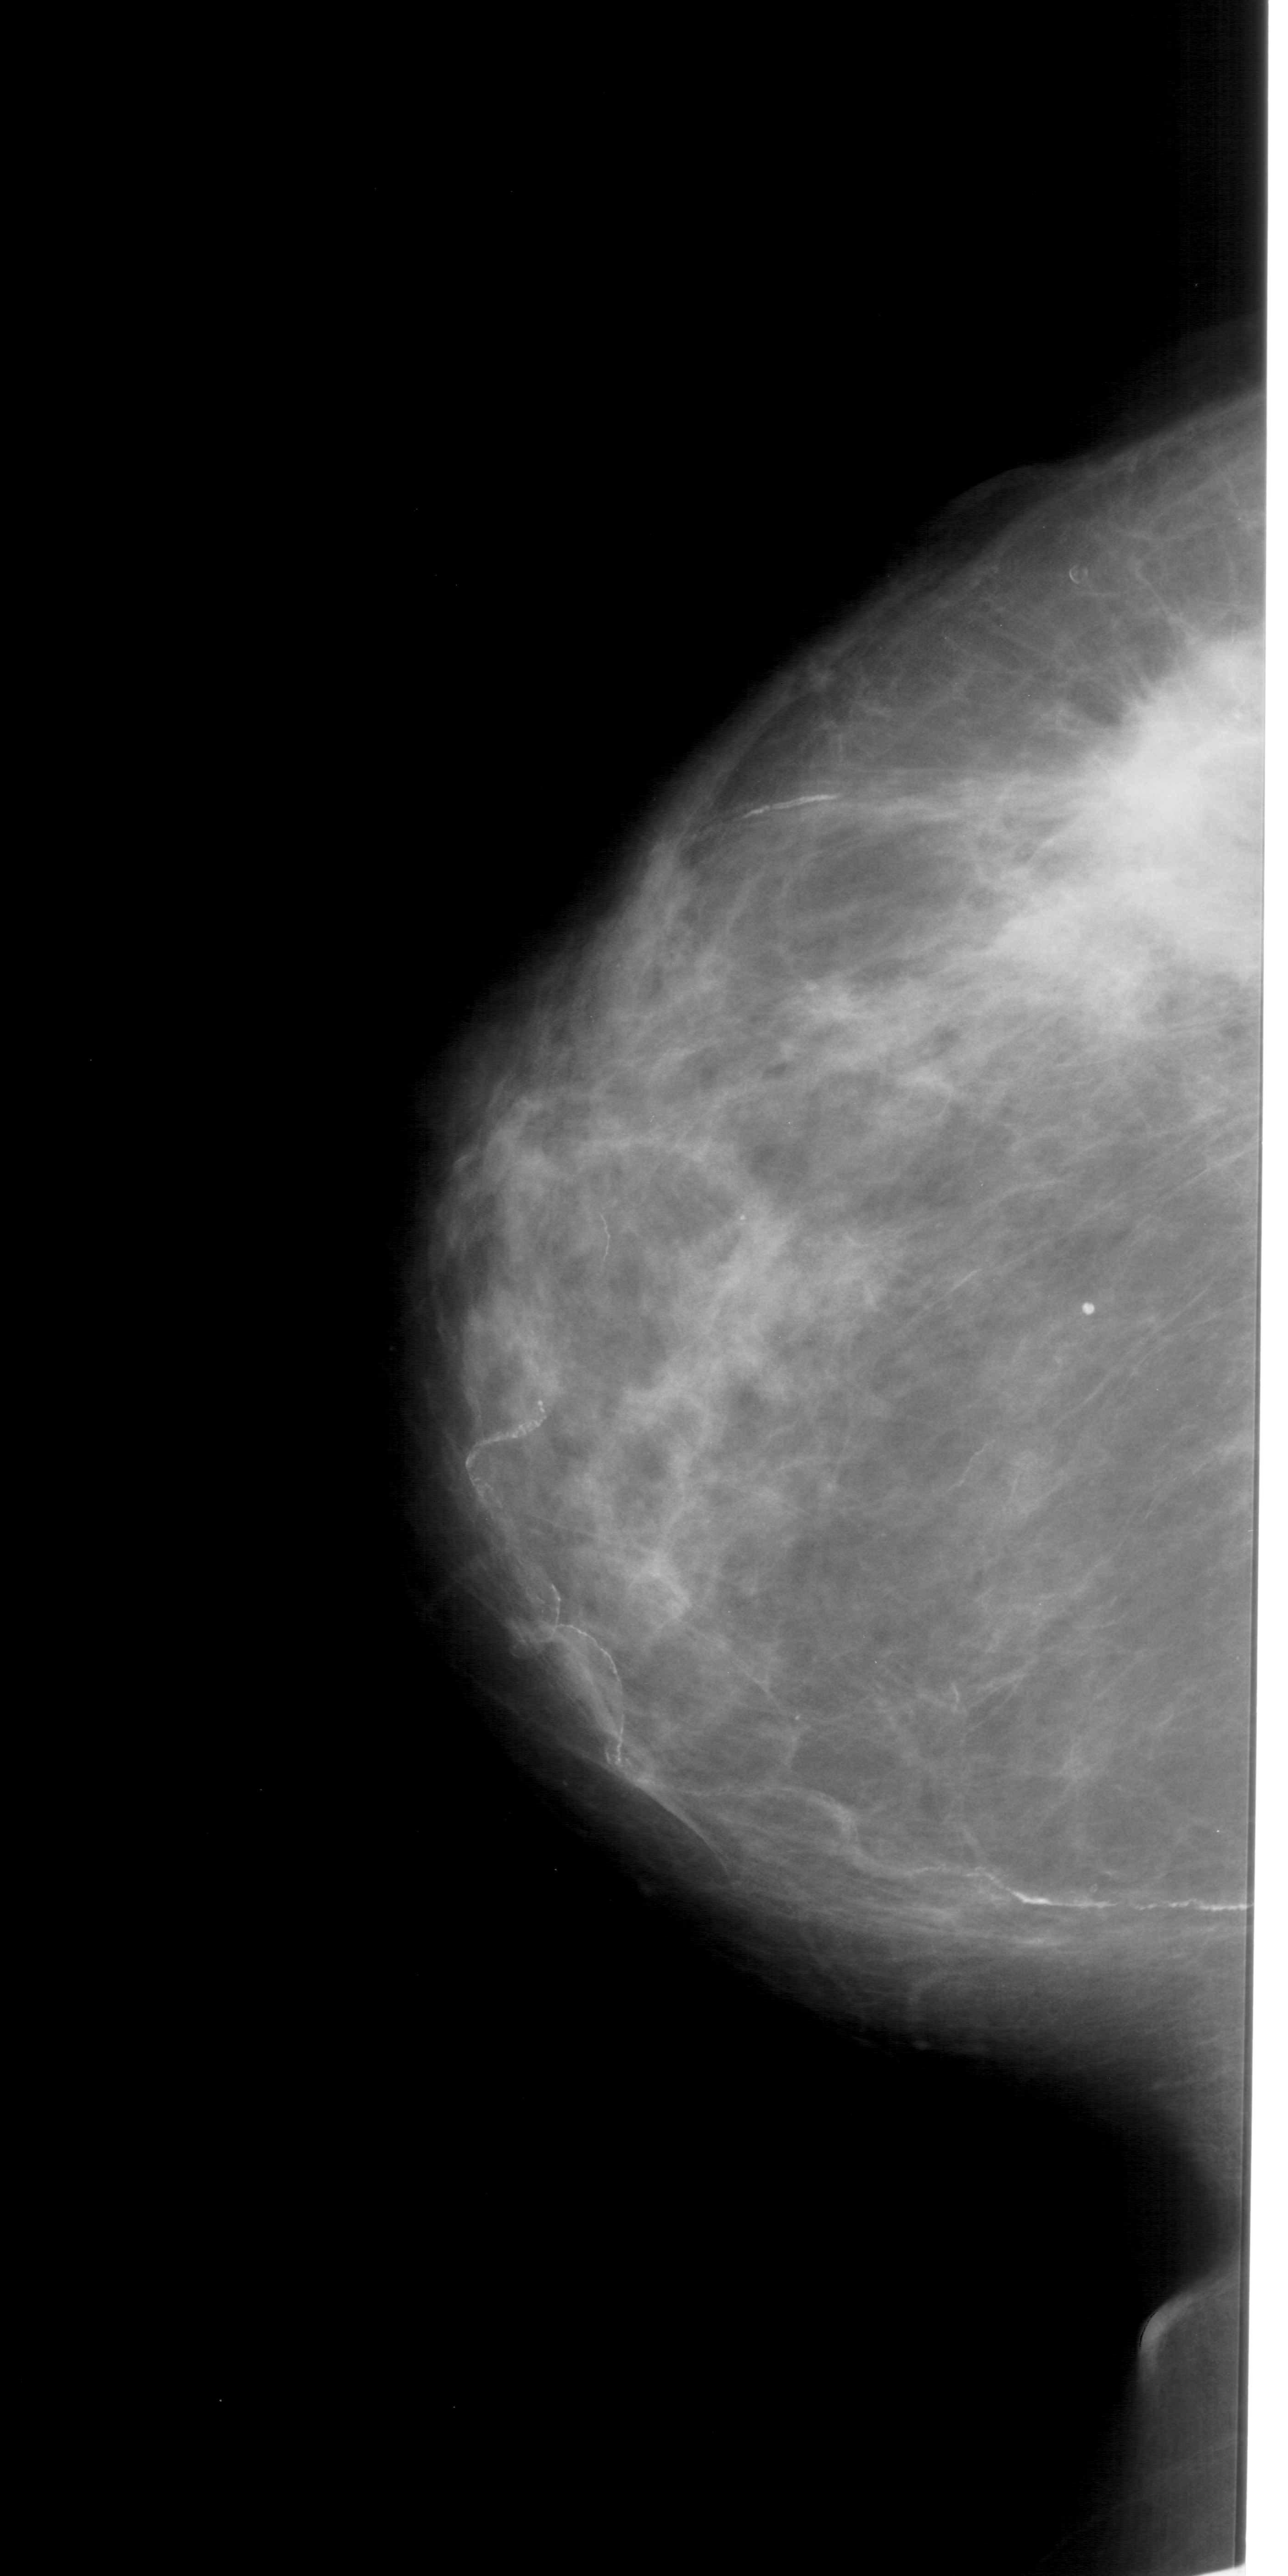
Mammogram (digitized film); left breast; craniocaudal (CC) view; BI-RADS breast density category 3 (scale 1–4); 1288 × 2576 image matrix.
Expert-marked regions of interest on this film, with their recorded descriptors:
- mass, shape irregular, margins spiculated; BI-RADS assessment category 5; subtlety rating 5 on a 1 (subtle) to 5 (obvious) scale; pathology (as recorded): malignant: box from (x=1001, y=617) to (x=1288, y=1012) px